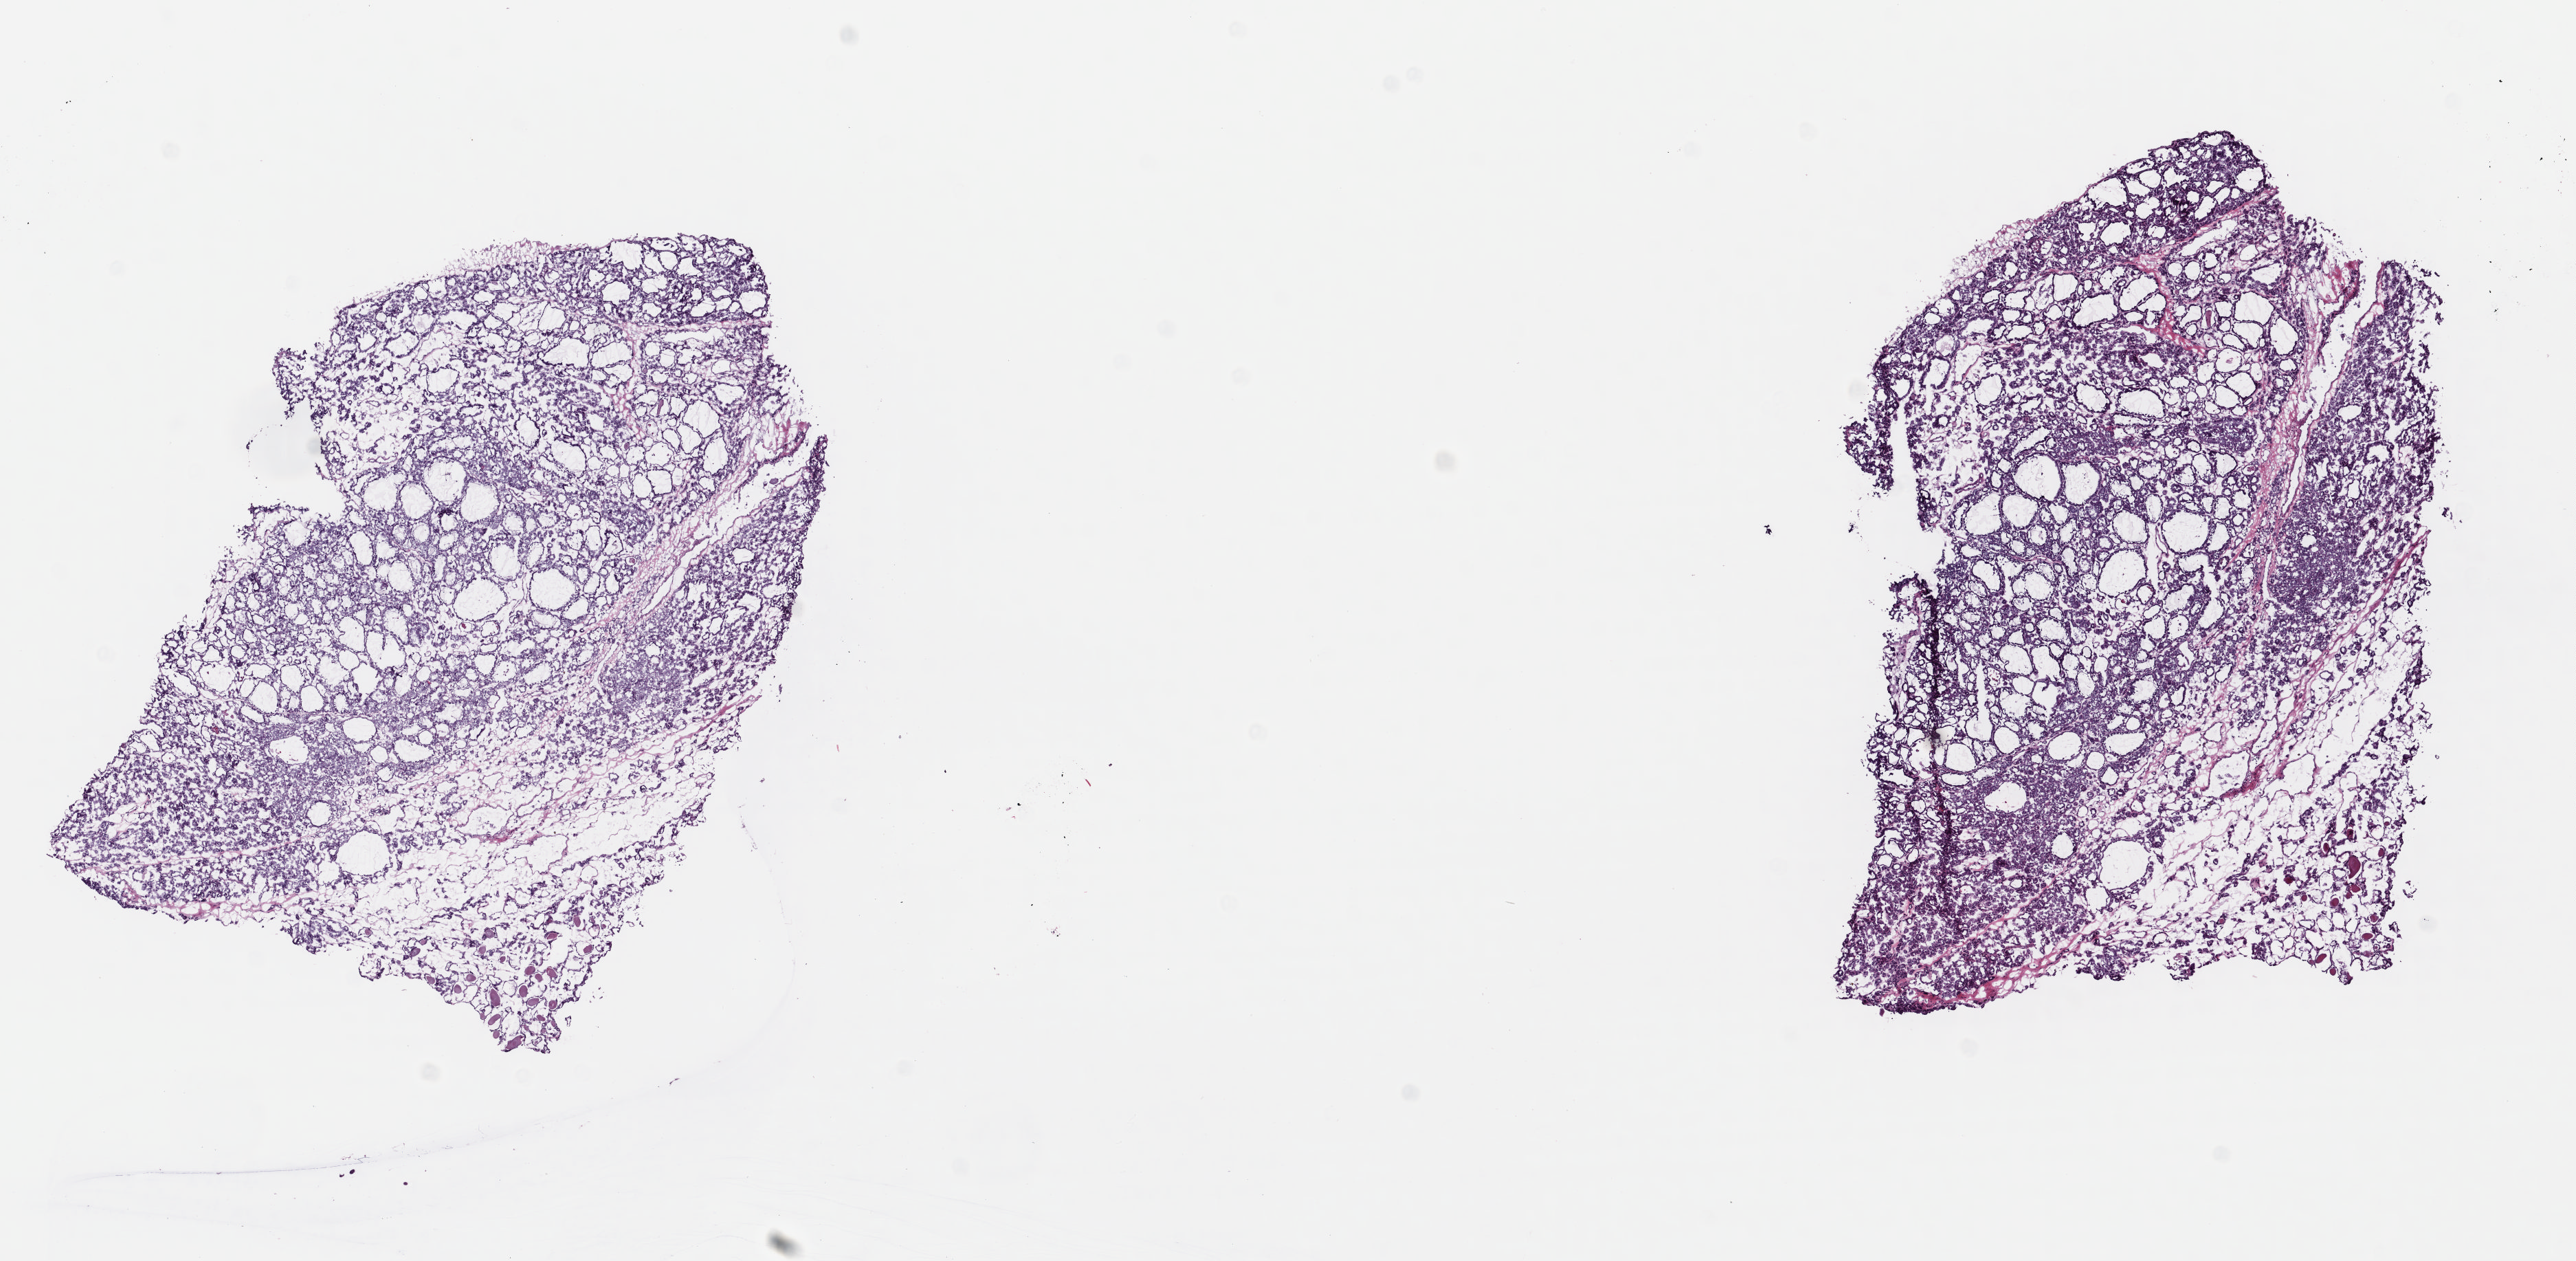
Whole-slide histology image, Hematoxylin and eosin (H&E) stained — whole scanned area (about 14.7 x 7.2 mm) shown as a low-resolution overview; frozen section from the top of the tissue portion; thyroid, primary tumour sample. Female, age 74 years at initial diagnosis. Pathologist review of this section (percent, as recorded): tumour cells 80%, tumour nuclei 90%, normal cells 10%, stromal cells 10%, necrosis 0%. Inflammatory infiltration, as recorded: lymphocyte infiltration 0%, monocyte infiltration 2%, neutrophil infiltration 0%.
- AJCC pathologic stage: II (7th edition)
- laterality: right
- histologic diagnosis: Papillary carcinoma, follicular variant (thyroid gland)